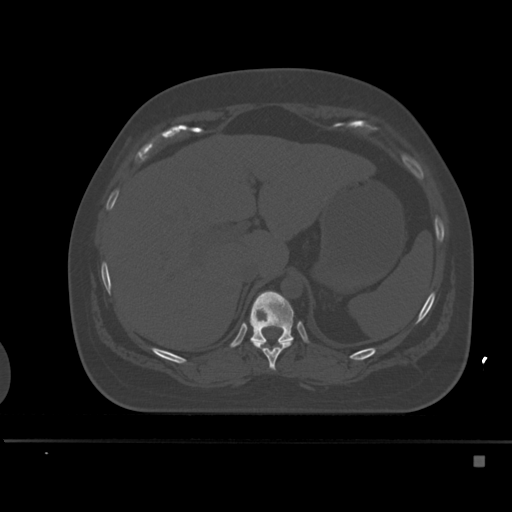
CT including the spine, one axial slice; position 239 of 495 along the scan axis; bone window (W 1800 / L 400 HU); 512 × 512 image matrix, field of view 404 × 404 mm. Patient: female, 33 years. From the clinical record (not read from this slice): primary cancer: breast.
Annotated regions visible in this slice (semi-automatically segmented with operator editing):
- T10 vertebra: bounding box <250,340,293,370> (left, top, right, bottom; pixels)
- T11 vertebra: <250,291,294,343>